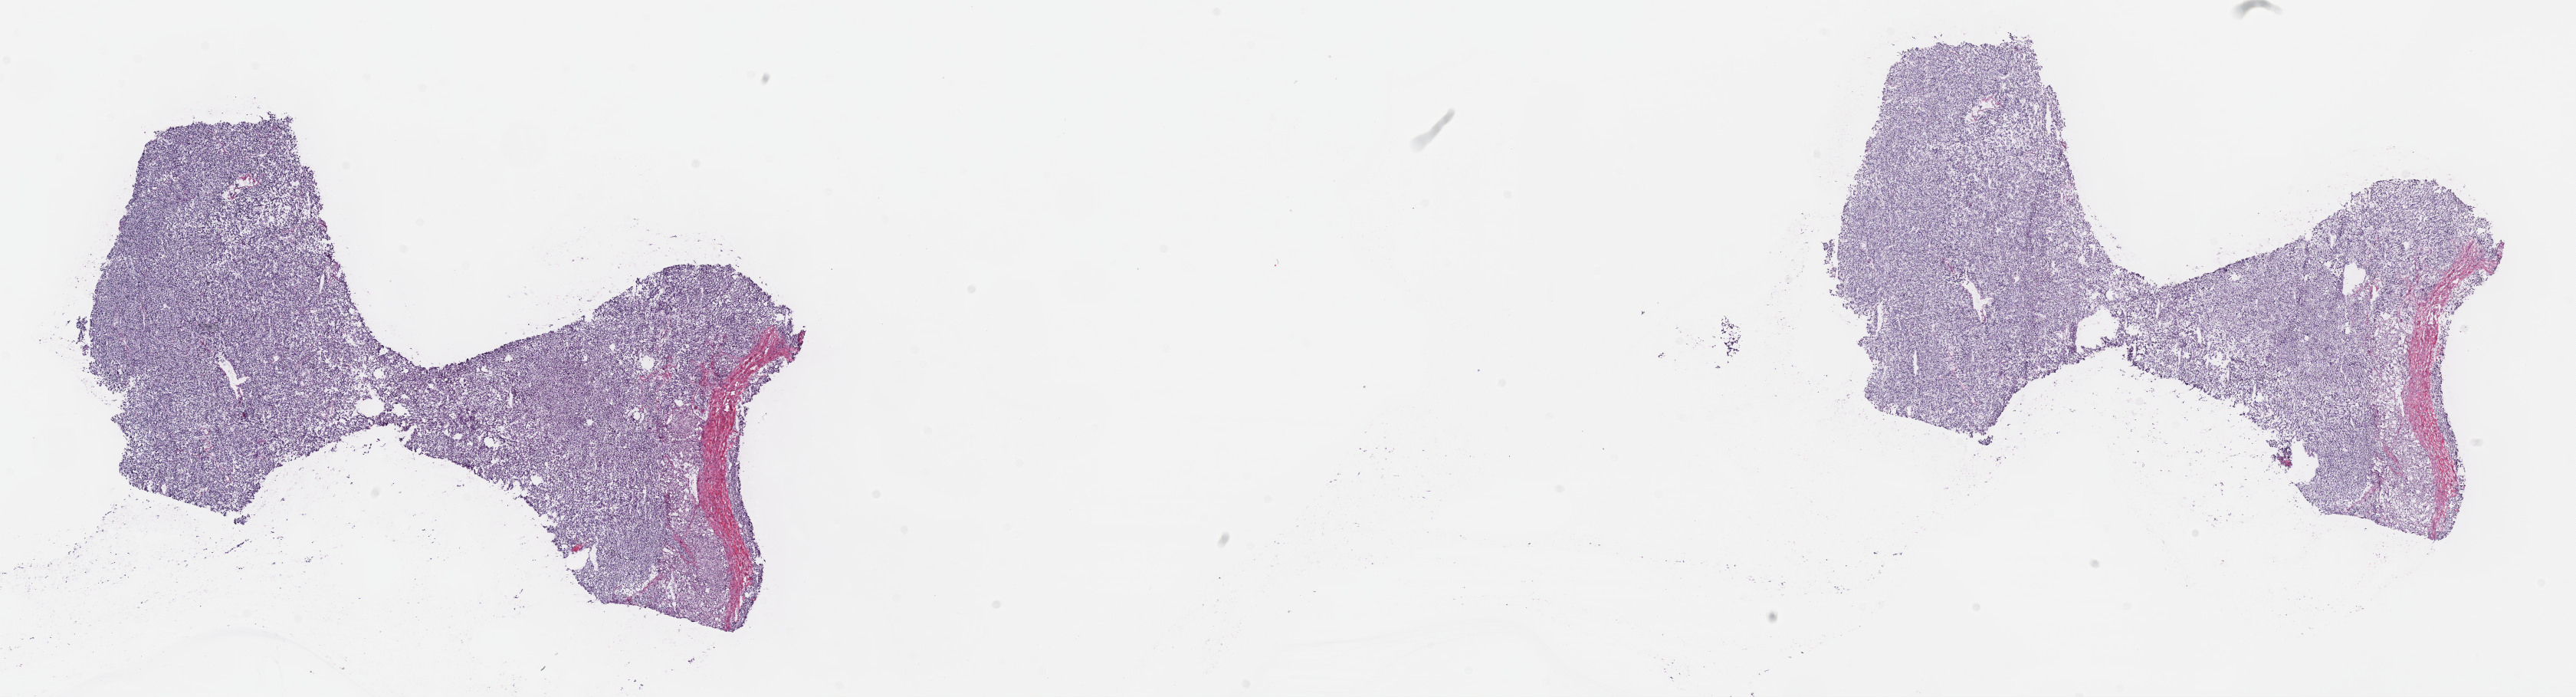
Whole-slide histology image, Hematoxylin and eosin (H&E) stained — a low-resolution overview of the entire scanned area, about 27.2 x 7.4 mm; frozen section; primary tumour sample from the adrenal gland. Patient: female, age at initial diagnosis 65 years. Composition of this section per pathologist review: tumour cells 80%, tumour nuclei 80%, normal cells 5%, stromal cells 15%, necrosis 0%. Infiltration values recorded for this section: lymphocyte infiltration 0%, monocyte infiltration 0%, neutrophil infiltration 0%.
- pathologic diagnosis: Pheochromocytoma, malignant
- laterality: left